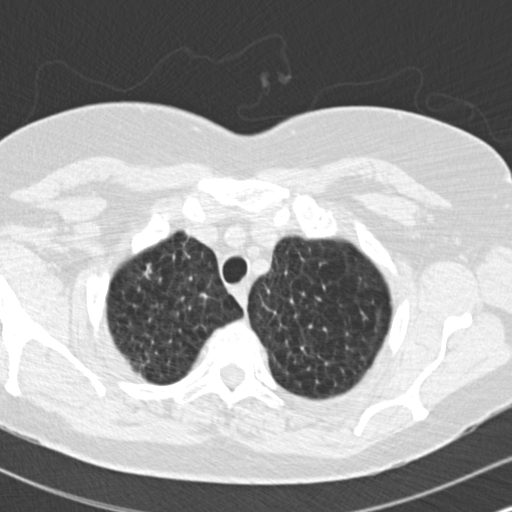
Axial slice from a low-dose chest CT screening exam, baseline annual screen, lung window (W 1500 / L -600 HU), 2 mm slice thickness, standard (soft-tissue) reconstruction kernel (B30f), 512 × 512 image matrix. Female participant, aged 73 years at enrolment. Former smoker at enrolment.
• Expert-annotated lung lesion, box from (x=126, y=252) to (x=170, y=290) px.
• The screening reader recorded 2 non-calcified nodules or masses ≥4 mm on this exam (right upper lobe, right upper lobe); which of them this box marks is not recorded.
• Official screen result: positive, change unspecified: nodule(s) >= 4 mm or enlarging nodule(s), mass(es), or other non-specific abnormalities suspicious for lung cancer.
• Participant outcome: lung cancer diagnosed 601 days after this screen (after the second annual screen) — adenocarcinoma, NOS, right upper lobe, moderately differentiated (G2), stage IB (AJCC 6th edition), 15 mm at pathology.